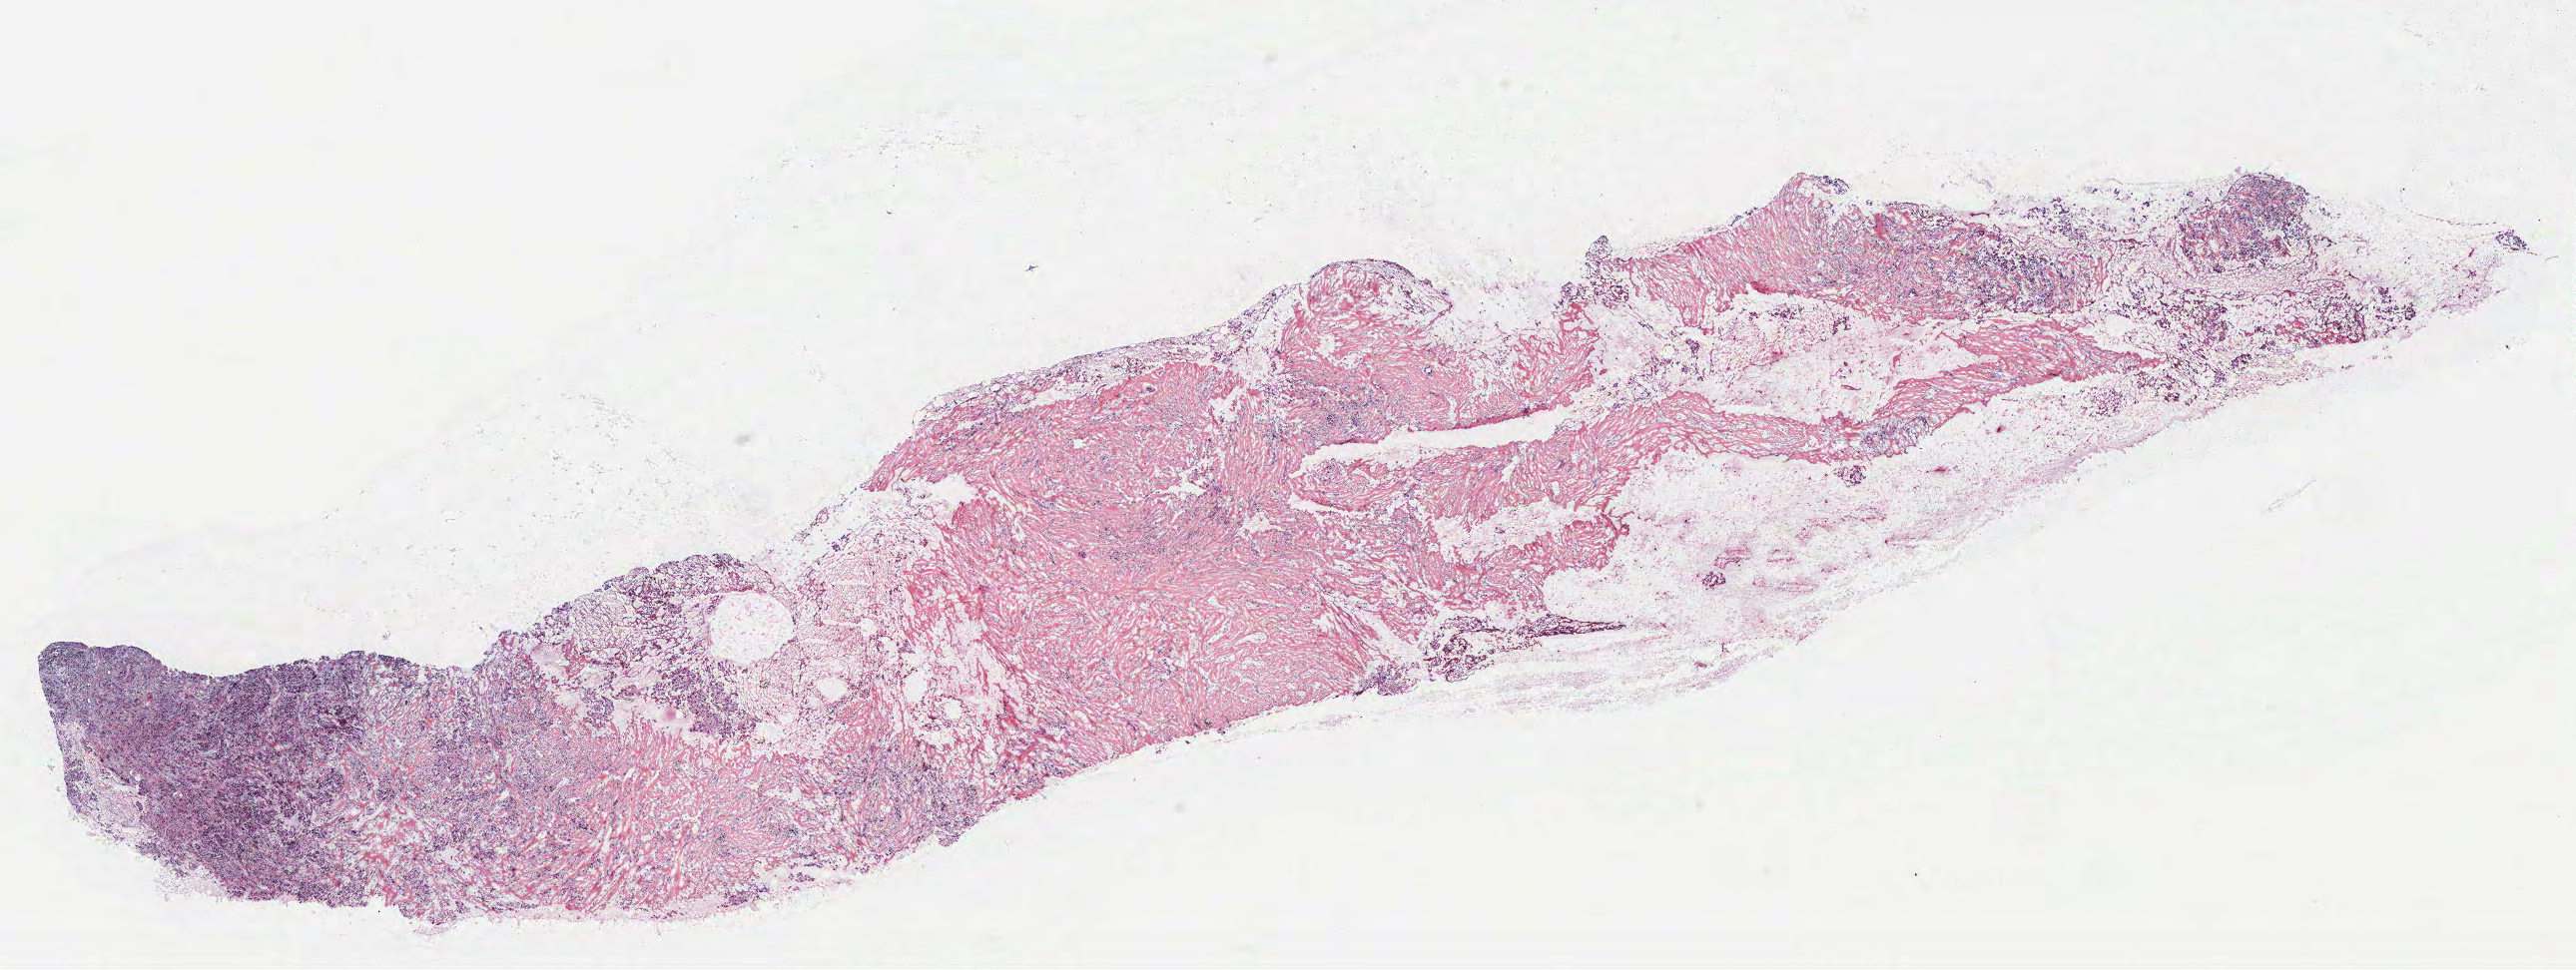
Digitized Hematoxylin and eosin (H&E) stained tissue section (whole slide), shown as a low-resolution overview of the whole scanned area (about 20.6 x 7.8 mm, from a 40x scan). Female, 65 y/o.
Specimen: tumour tissue sample, breast.